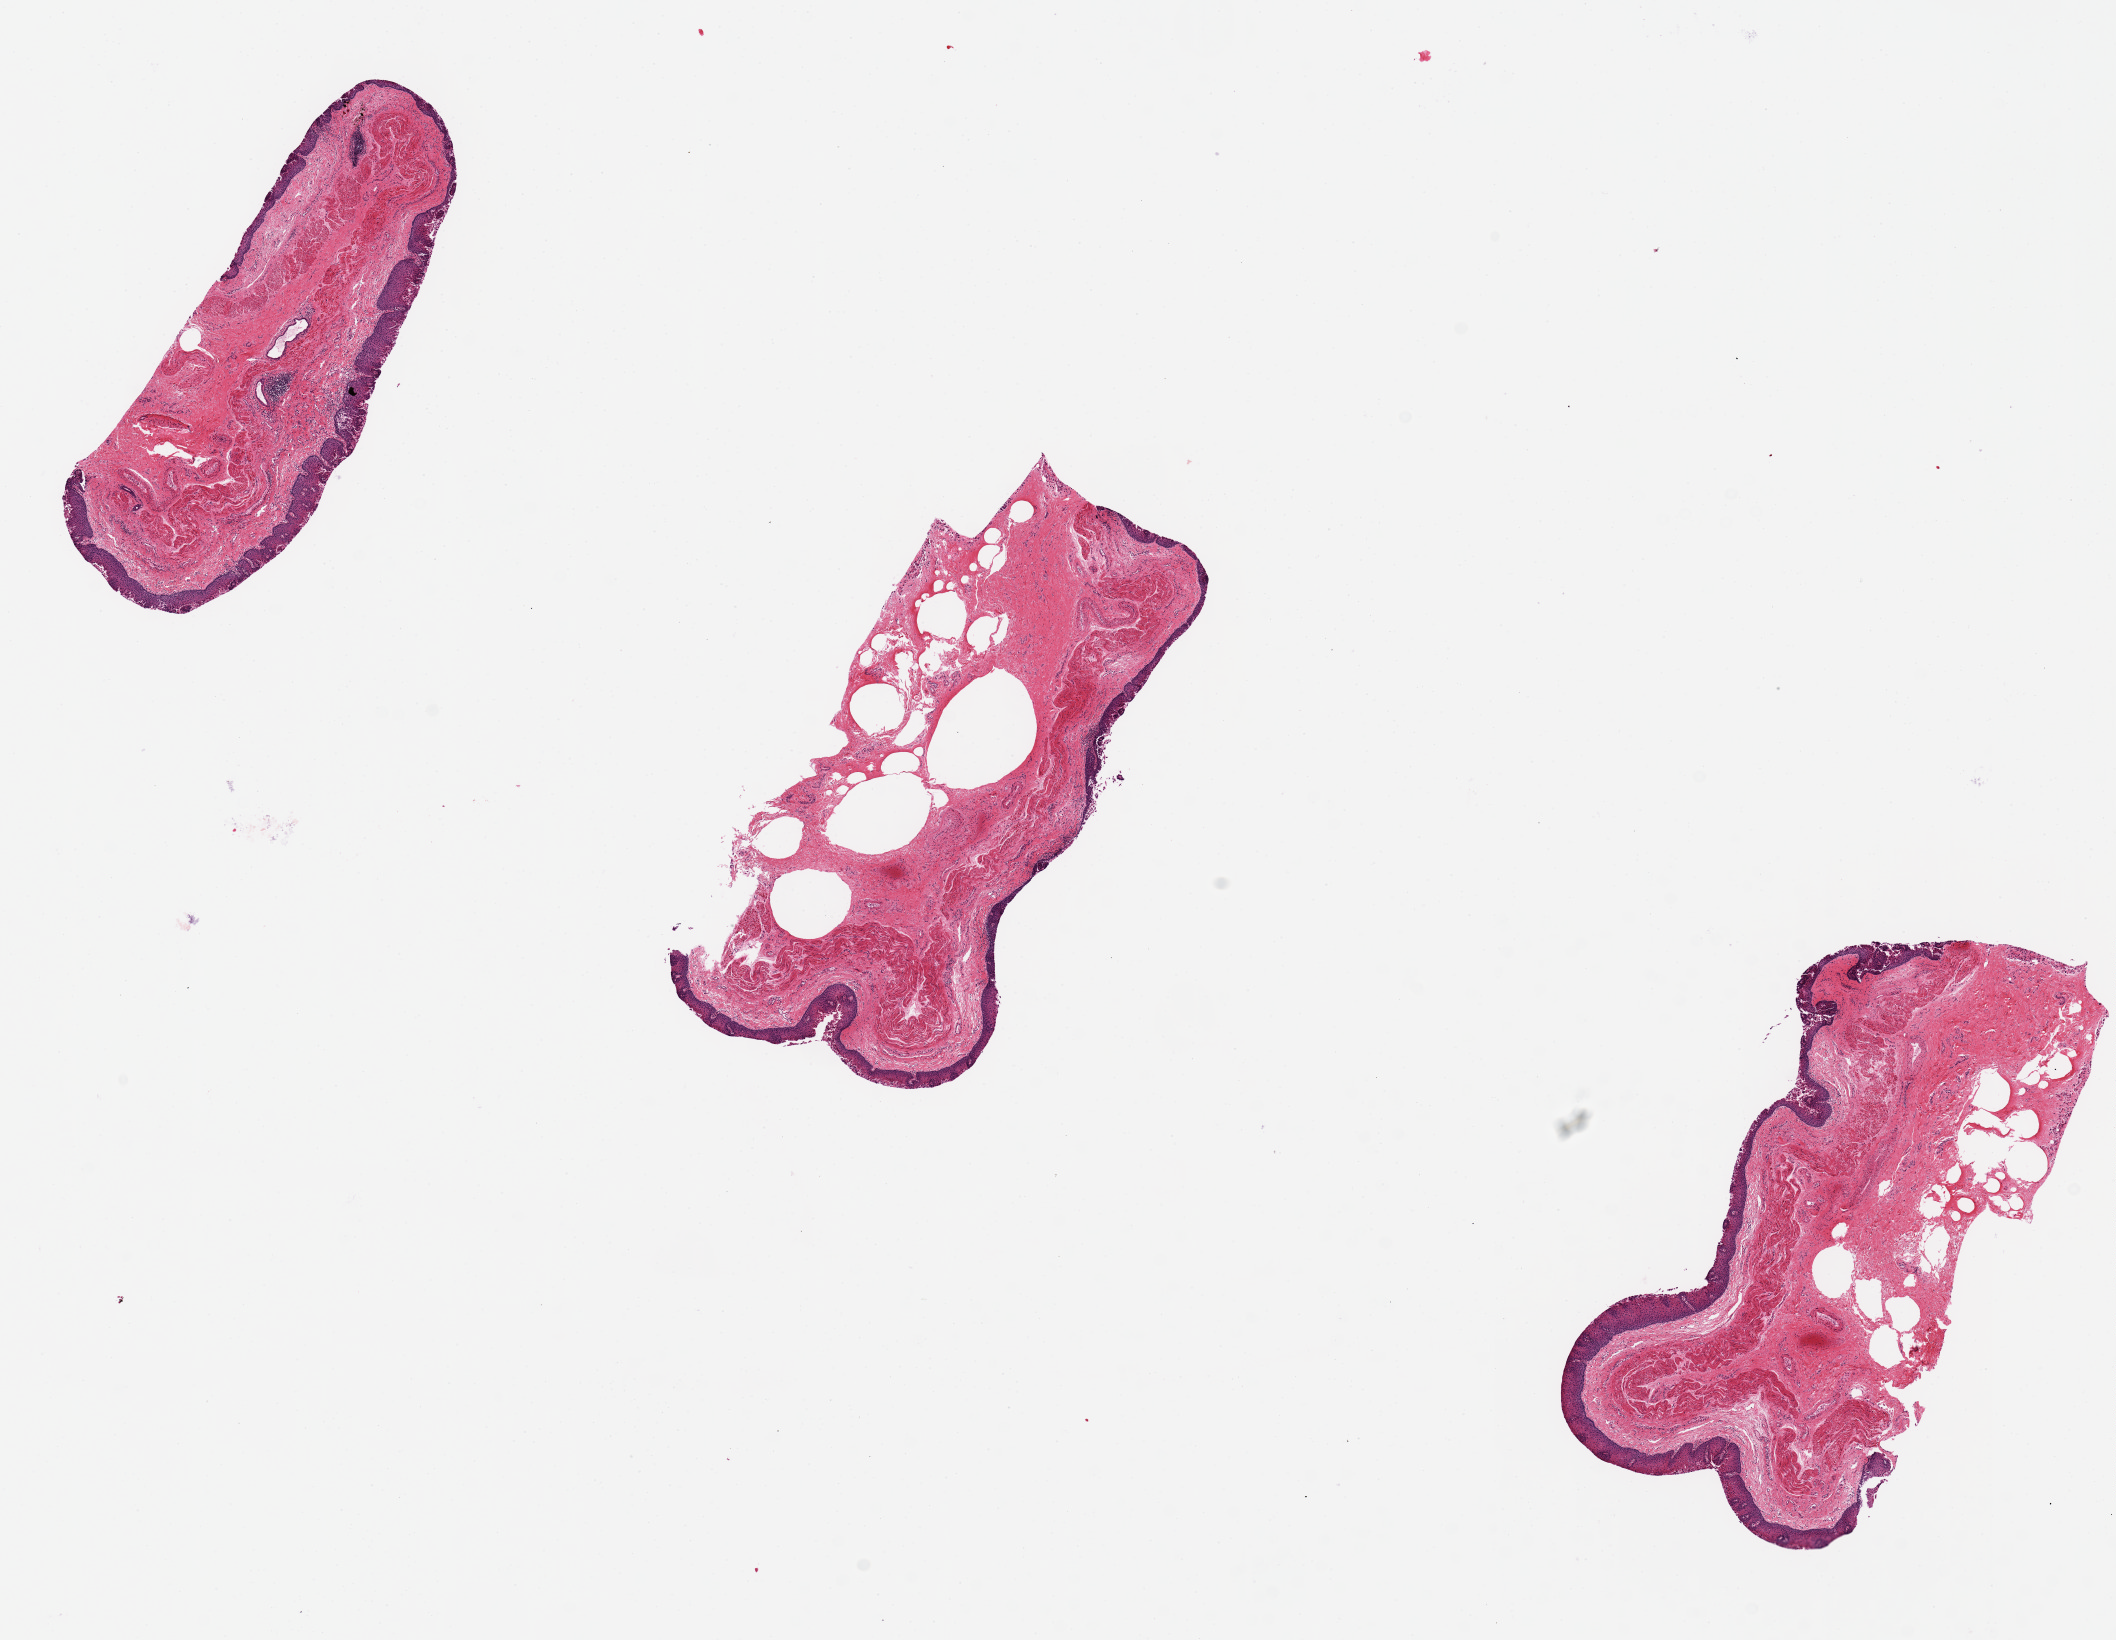
Whole-slide image, haematoxylin and eosin stain, whole scanned area (about 16.7 x 13.0 mm) shown as a low-resolution overview; PAXgene-fixed, paraffin-embedded tissue; target tissue: esophageal mucous membrane; tissue donor sample. Donor: male.
Reviewer comment on this tissue sample: Epithelial thickness is approx 15% of total thickness of specimen.